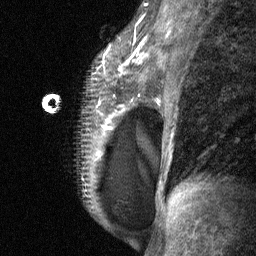
Breast MRI (dynamic contrast-enhanced), one sagittal slice; slice 45 of 64 in the series (ordered by position); dynamic contrast-enhanced study with each time point stored as its own series, time point 2 of 3 at this slice position (early post-contrast, ordered by acquisition time); 1.5 T; TE 4.8 ms, TR 27 ms; 2 mm slice thickness; 256 × 256 image matrix. Patient: female, 34 years. Case-level facts recorded for this patient, not image findings: setting: breast cancer imaged before/during neoadjuvant chemotherapy; receptor status: HR-positive, HER2-negative.
Outlined on this slice (semi-automatic segmentation, software-assisted and operator-edited):
- analysis volume of interest (the breast-tissue region the enhancement analysis was run in; not a lesion): bounding box [x1, y1, x2, y2] px = [41, 23, 157, 197]
- tumour enhancement mask (voxels above the 90 % enhancement threshold inside the analysis volume of interest): [103, 47, 142, 130]